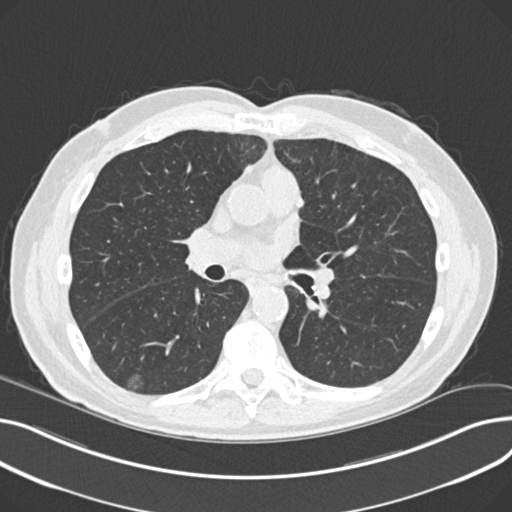
Low-dose screening chest CT, axial slice; third screening round (two years after baseline); lung window (W 1500 / L -600 HU); 2 mm slice thickness; standard (soft-tissue) reconstruction kernel (B30f); 120 kVp; slice 112 of 230 in the series. Male participant, aged 68 years at enrolment. Current smoker at enrolment.
Lesion marked by an expert reader, bounding box <123,365,156,398> (left, top, right, bottom; pixels). The screening reader recorded 5 non-calcified nodules or masses ≥4 mm on this exam (right upper lobe, left upper lobe, right upper lobe, right lower lobe, right upper lobe); which of them this box marks is not recorded. Official screen result: positive, other.